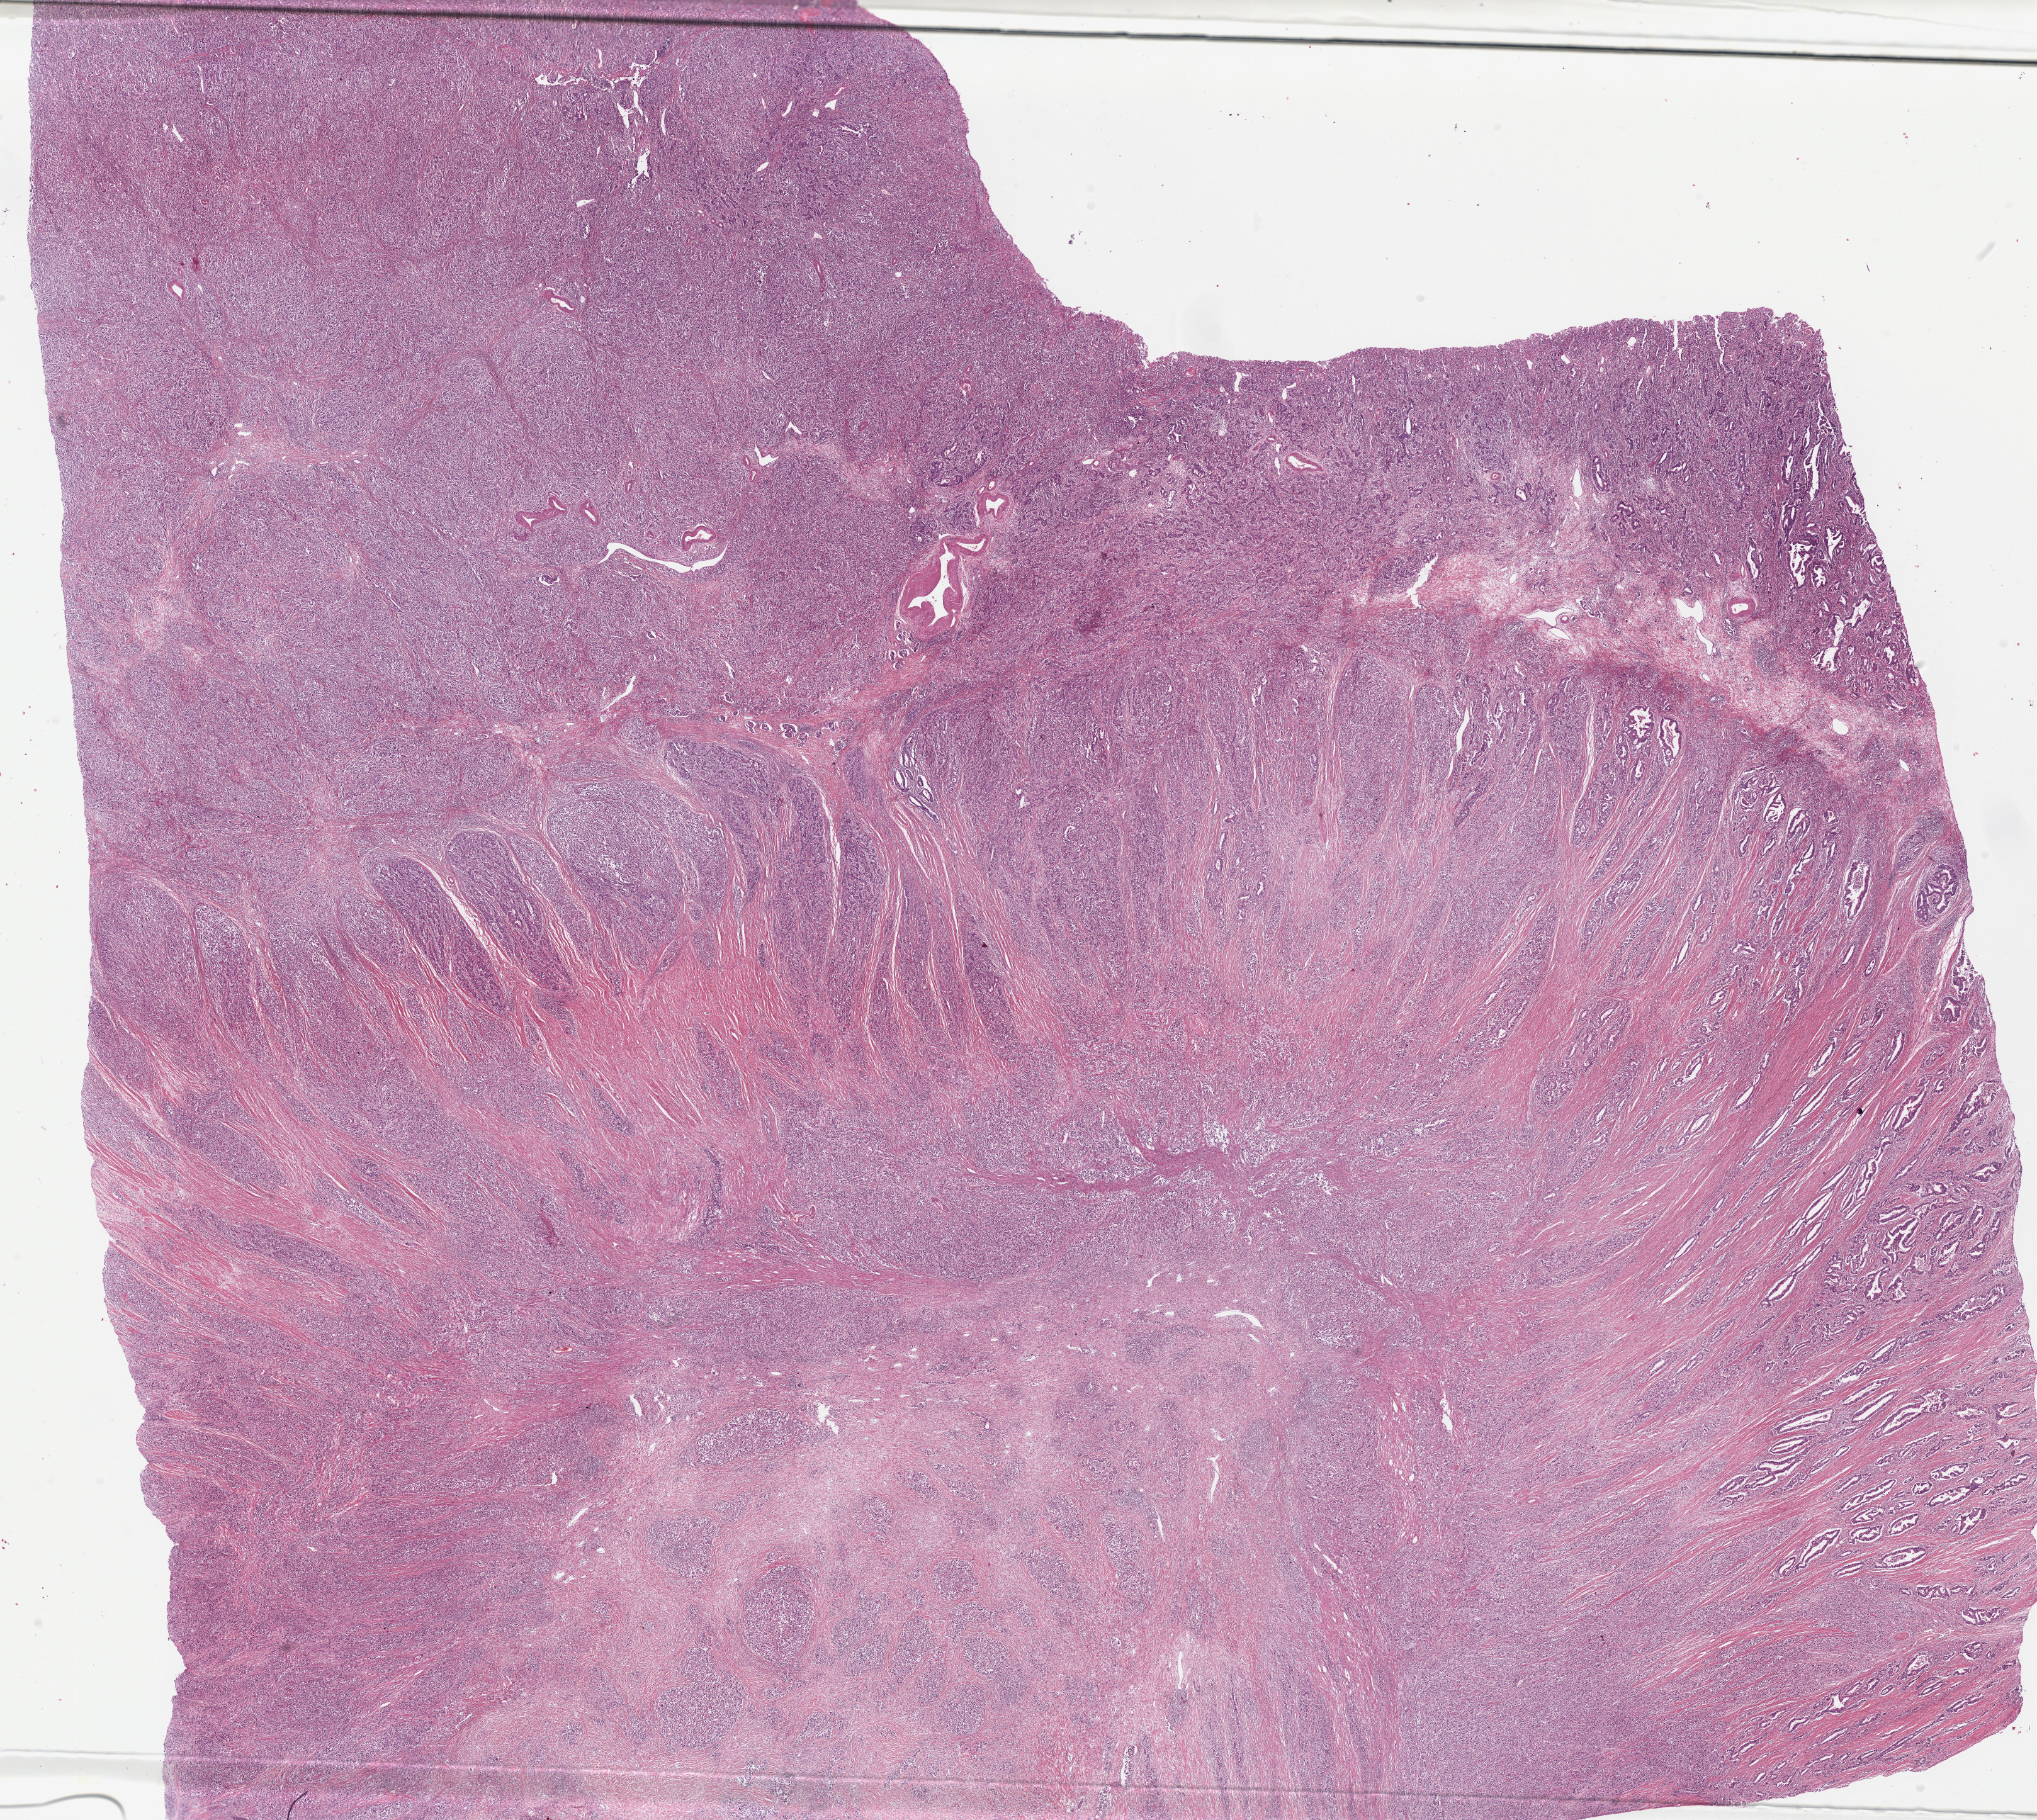
Whole-slide histology image, H&E — shown as a low-resolution overview of the whole scanned area (about 25.6 x 22.9 mm). Formalin-fixed paraffin-embedded (FFPE) diagnostic section. Stomach, primary tumour sample. Male, age 72 years at initial diagnosis. Histologic grade: G3 (poorly differentiated).
• lymph nodes positive (case pathology): 49 of 89 examined
• histologic diagnosis: Carcinoma, diffuse type (body of stomach)
• AJCC pathologic stage: IIIC (7th edition)